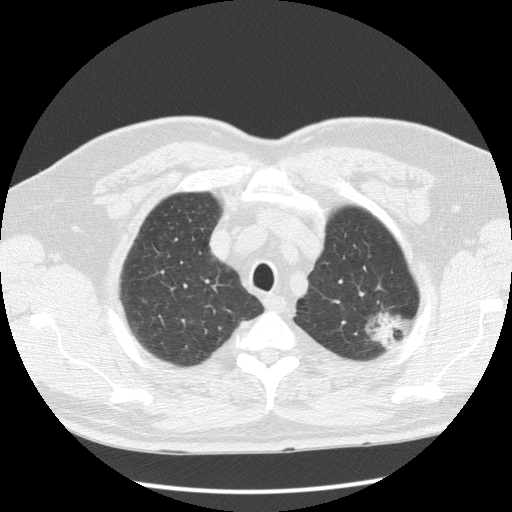
Low-dose screening chest CT, axial slice. Baseline screening round. Lung window (W 1500 / L -600 HU). 2.5 mm slice thickness. Slice 20 of 123 in the series. Male, age 60 years at enrolment. Current smoker at enrolment.
Lesion marked by an expert reader, box from (x=353, y=296) to (x=415, y=357) px. The screening reader recorded 3 non-calcified nodules or masses ≥4 mm on this exam; which of them this box marks is not recorded. Later outcome: lung cancer diagnosed 48 days after this screen — bronchiolo-alveolar adenocarcinoma, NOS, left upper lobe, well differentiated (G1), stage IA (AJCC 6th edition), 27 mm at pathology.